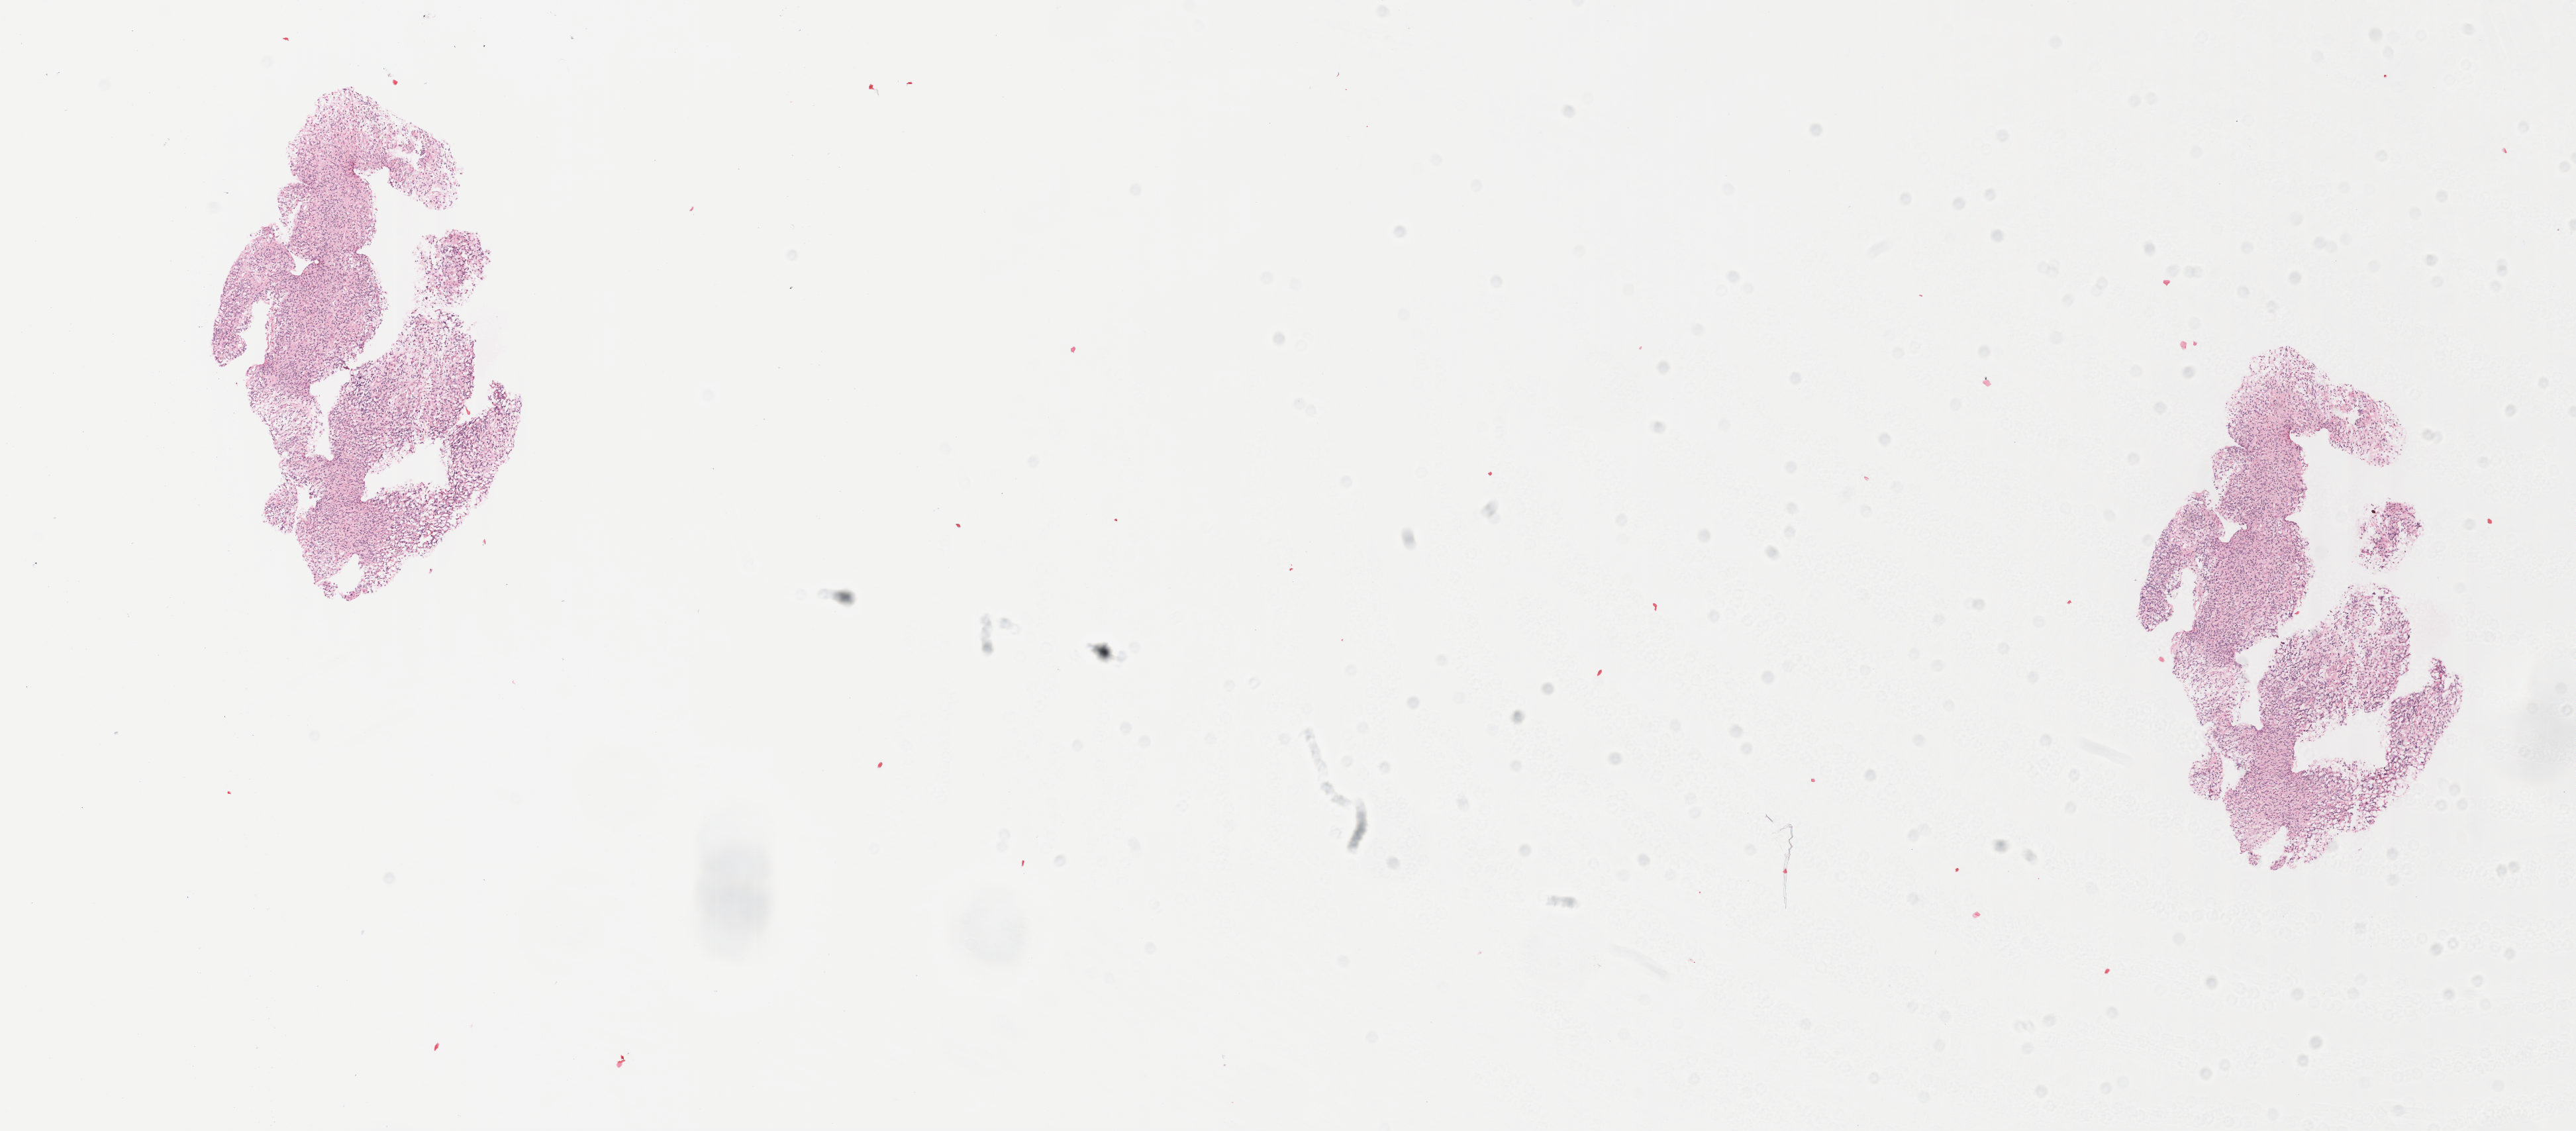
H&E whole-slide image — shown as a low-resolution overview of the whole scanned area (about 15.5 x 6.8 mm, acquisition: 40x scan); frozen section from the top of the tissue portion; brain, primary tumour sample. Male, age 40 years at initial diagnosis.
Pathologic diagnosis: Oligodendroglioma, anaplastic (cerebrum).